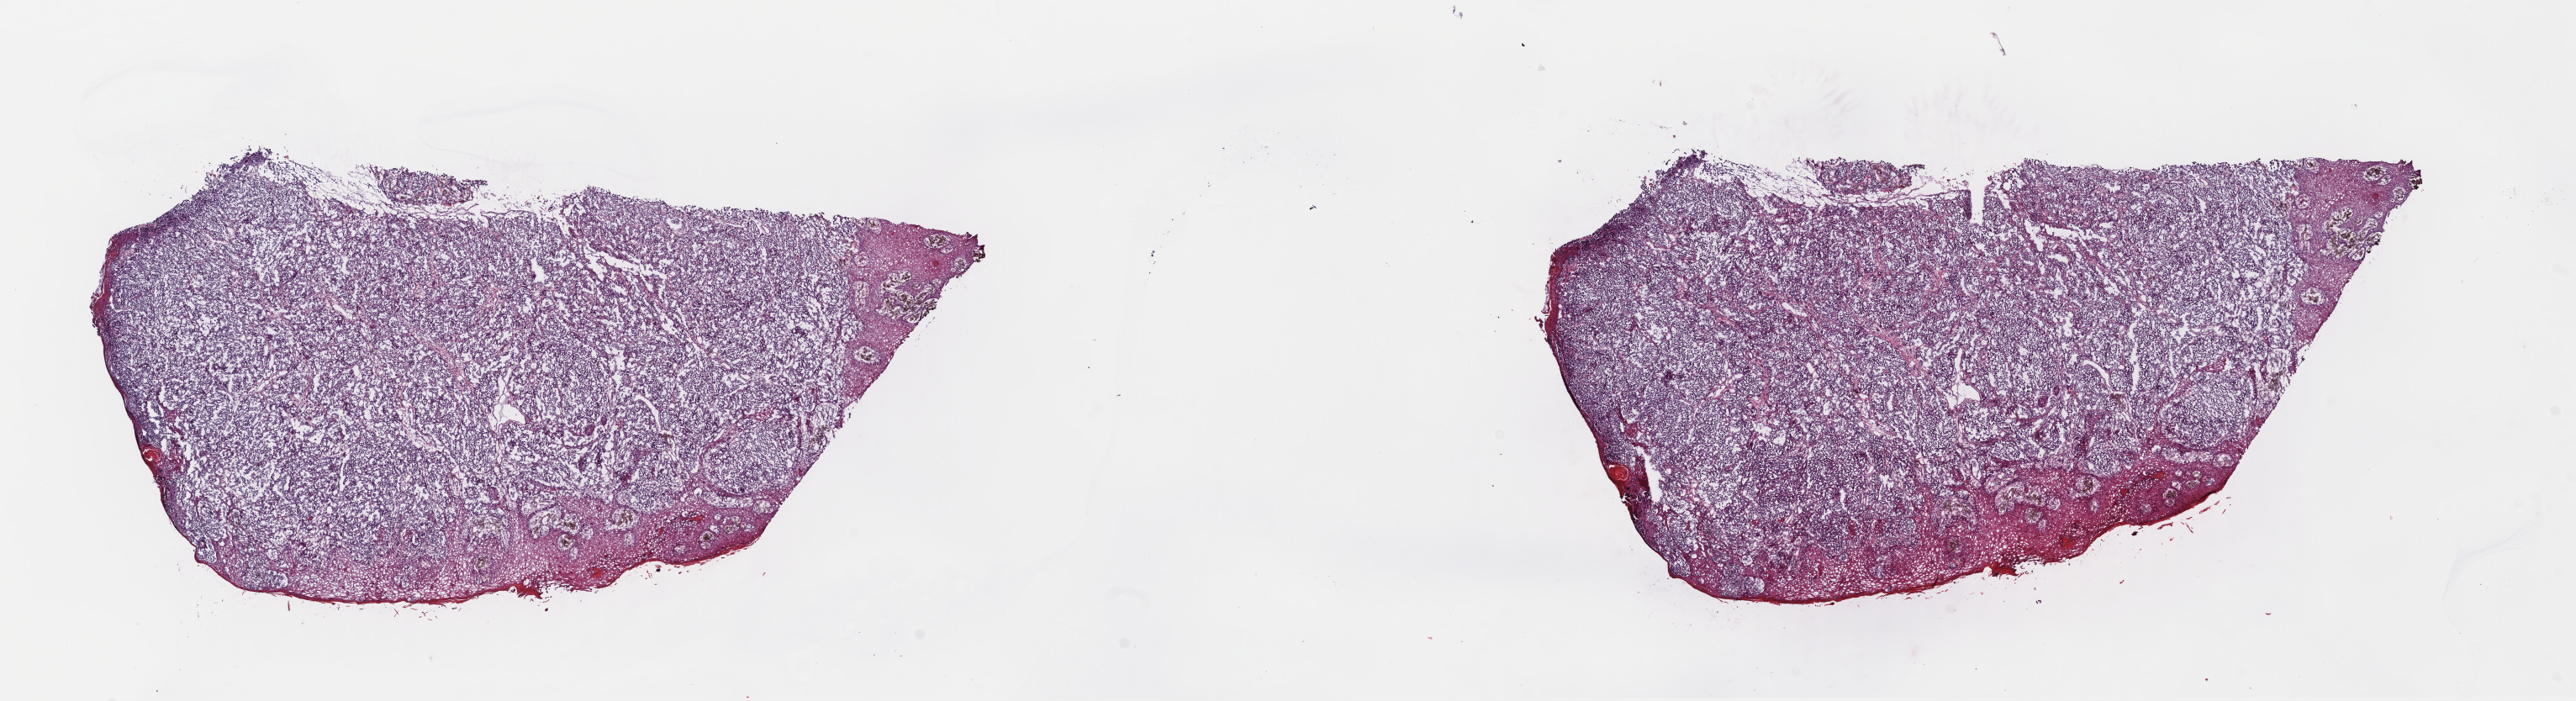
Hematoxylin and eosin (H&E) stained whole-slide image — whole scanned area (about 24.1 x 6.6 mm) shown as a low-resolution overview. Frozen section. Primary tumour sample from the skin. Patient: female, age at initial diagnosis 61 years. Slide review estimates, as recorded: tumour cells 85%, tumour nuclei 90%, normal cells 10%, stromal cells 5%, necrosis 0%. Inflammatory infiltration, as recorded: lymphocyte infiltration 8%, monocyte infiltration 0%, neutrophil infiltration 0%.
AJCC pathologic stage: IB (7th edition). Histologic diagnosis: Malignant melanoma, NOS. TNM: T2a NX M0.